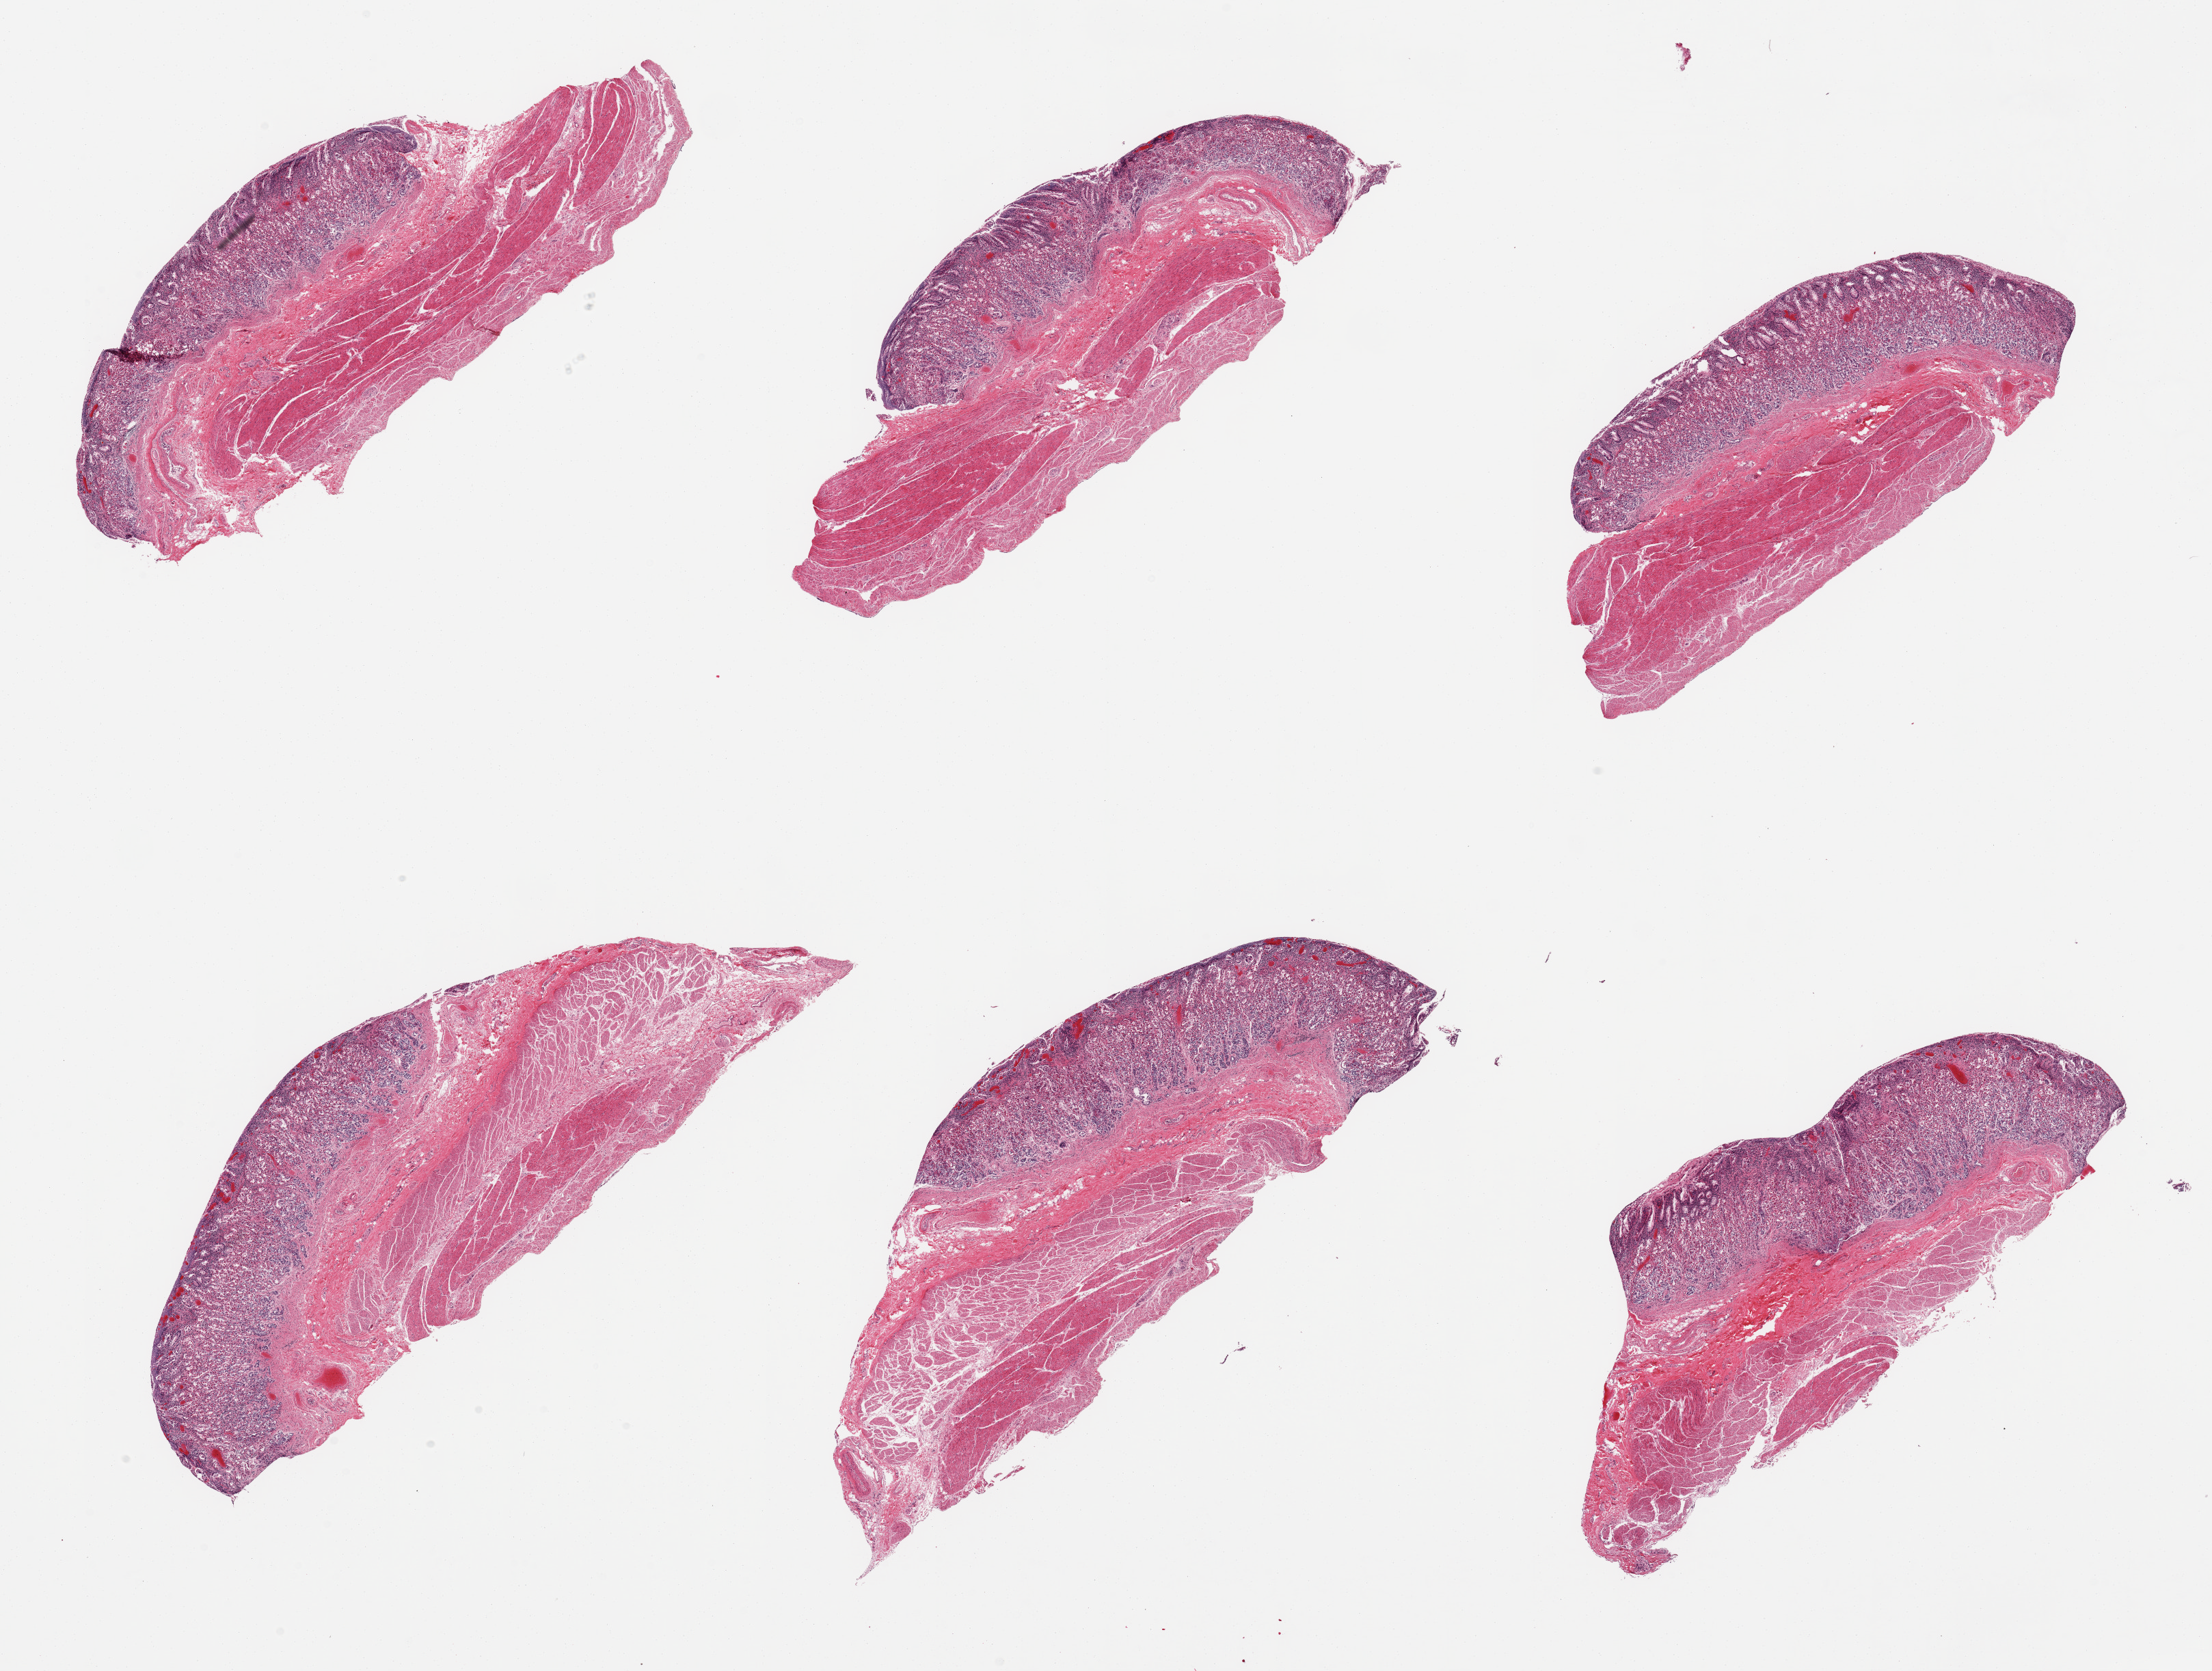
Whole-slide image, haematoxylin and eosin stain, whole scanned area (about 25.6 x 19.3 mm, slide scanned at 20x) shown as a low-resolution overview. PAXgene-fixed paraffin-embedded (PFPE) section. Target tissue: stomach. Tissue donor sample. Male donor.
Review note (as recorded): 6 pieces; chronic gastritis; chief and parietal mucosal cells identifiable, but dissociated.